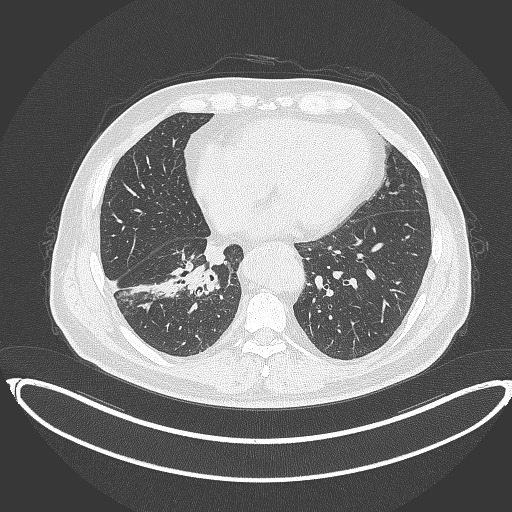
Chest CT, one axial slice; position 148 of 387 along the scan axis; 120 kVp; lung window (W 1500 / L -600 HU); 1 mm slice thickness; 512 × 512 image matrix, field of view 448 × 448 mm. Male patient, age 61 years. Case-level facts recorded for this patient, not image findings: clinical TNM (as recorded): T1b N1 M0.
Outlined on this slice (rectangle marked by the reading radiologist):
- lung tumour (recorded histology: squamous cell carcinoma): box from (x=183, y=263) to (x=222, y=297) px